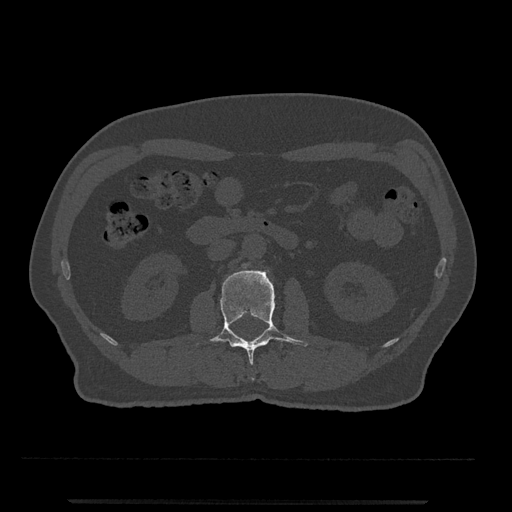
CT including the spine, one axial slice. Position 265 of 797 along the scan axis. Reconstruction kernel Br40s/3. 120 kVp. Bone window (W 1800 / L 400 HU). 0.5 mm slice thickness. 512 × 512 image matrix, field of view 419 × 419 mm. Patient: male, 63 years. Case-level facts recorded for this patient, not image findings: primary cancer: prostate.
Outlined on this slice (semi-automatic segmentation, software-assisted and operator-edited):
- L2 vertebra: box from (x=204, y=270) to (x=308, y=364) px